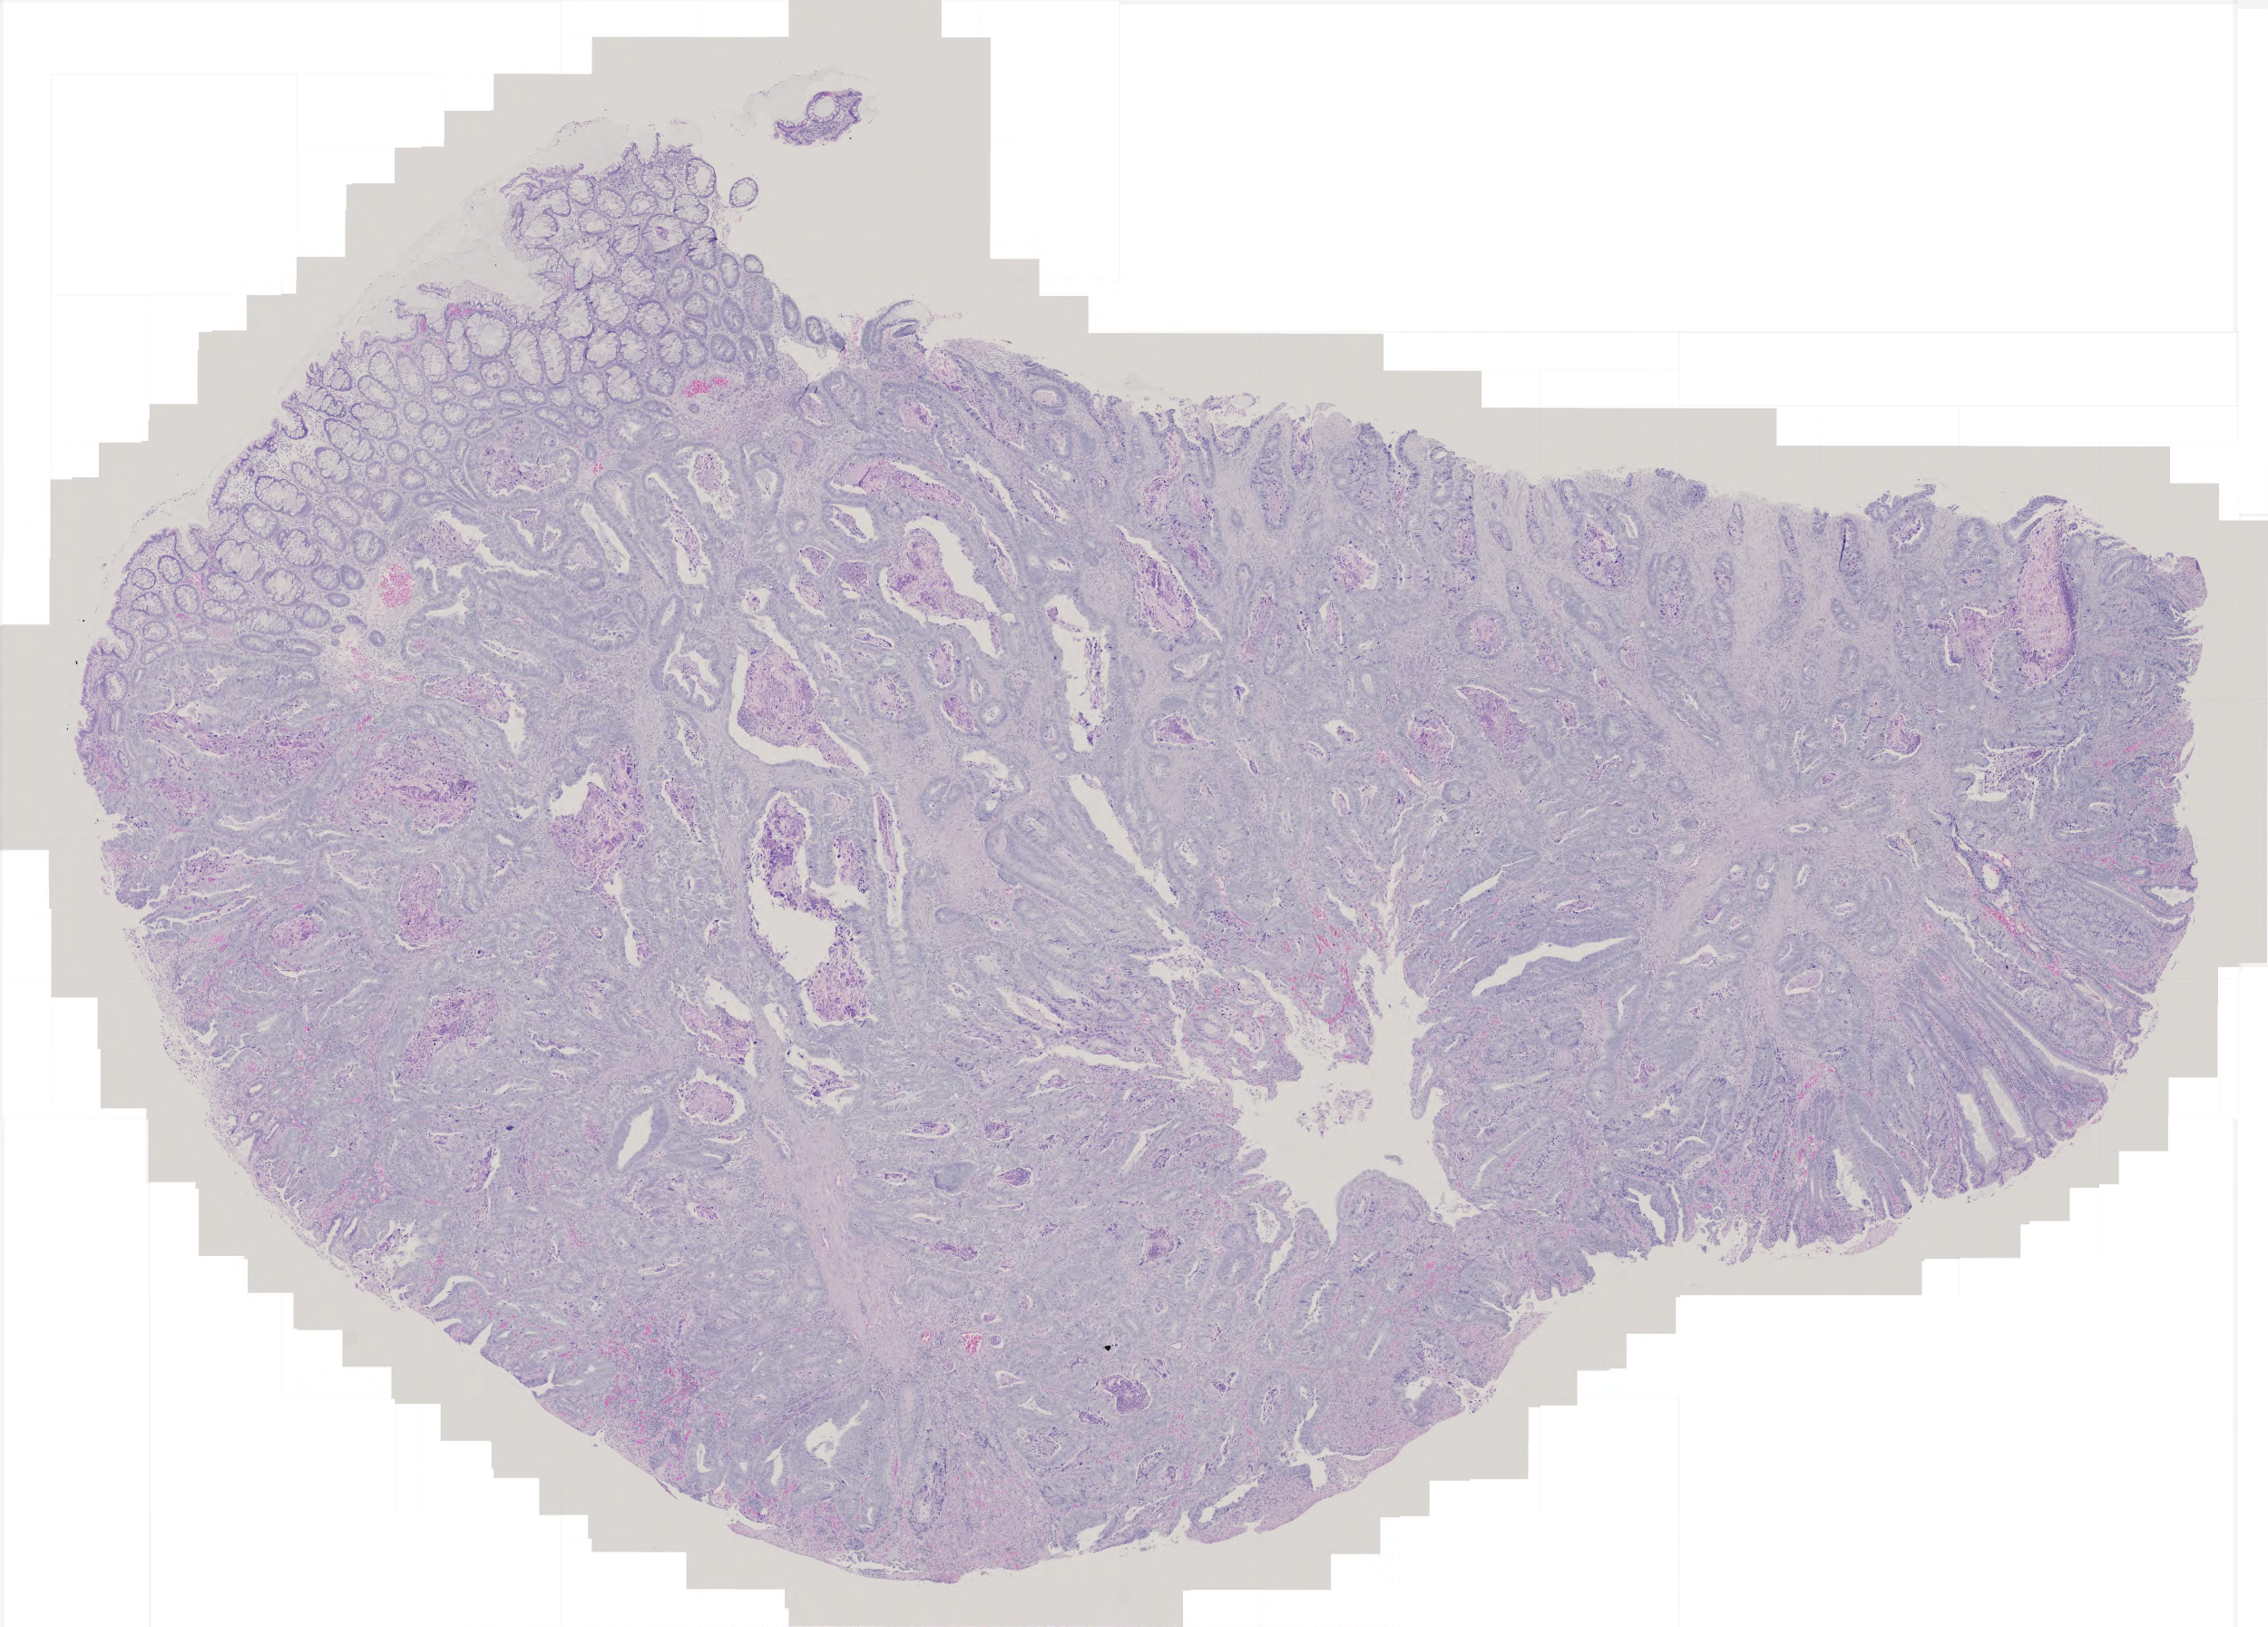
H&E whole-slide image, shown as a low-resolution overview of the whole scanned area (about 5.0 x 3.6 mm); formalin-fixed paraffin-embedded (FFPE) diagnostic section; primary tumour sample from the colon. Male, age 64 years at initial diagnosis.
Histologic diagnosis: Adenocarcinoma, NOS.